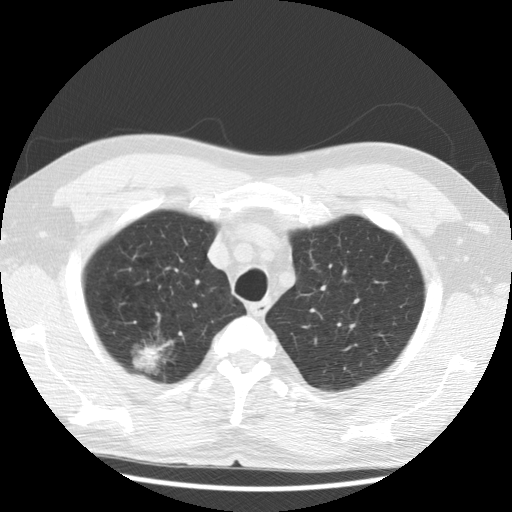
Low-dose screening chest CT, one axial slice. Slice 98 of 122 in the series (ordered by position). Reconstruction kernel STANDARD. Lung window (W 1500 / L -600 HU). 2.5 mm slice thickness. 512 × 512 image matrix, field of view 350 × 350 mm.
Annotated regions visible in this slice (expert manual segmentation):
- lesion 1 (tumor, upper lobe of right lung): bounding box <136,346,158,371> (left, top, right, bottom; pixels)